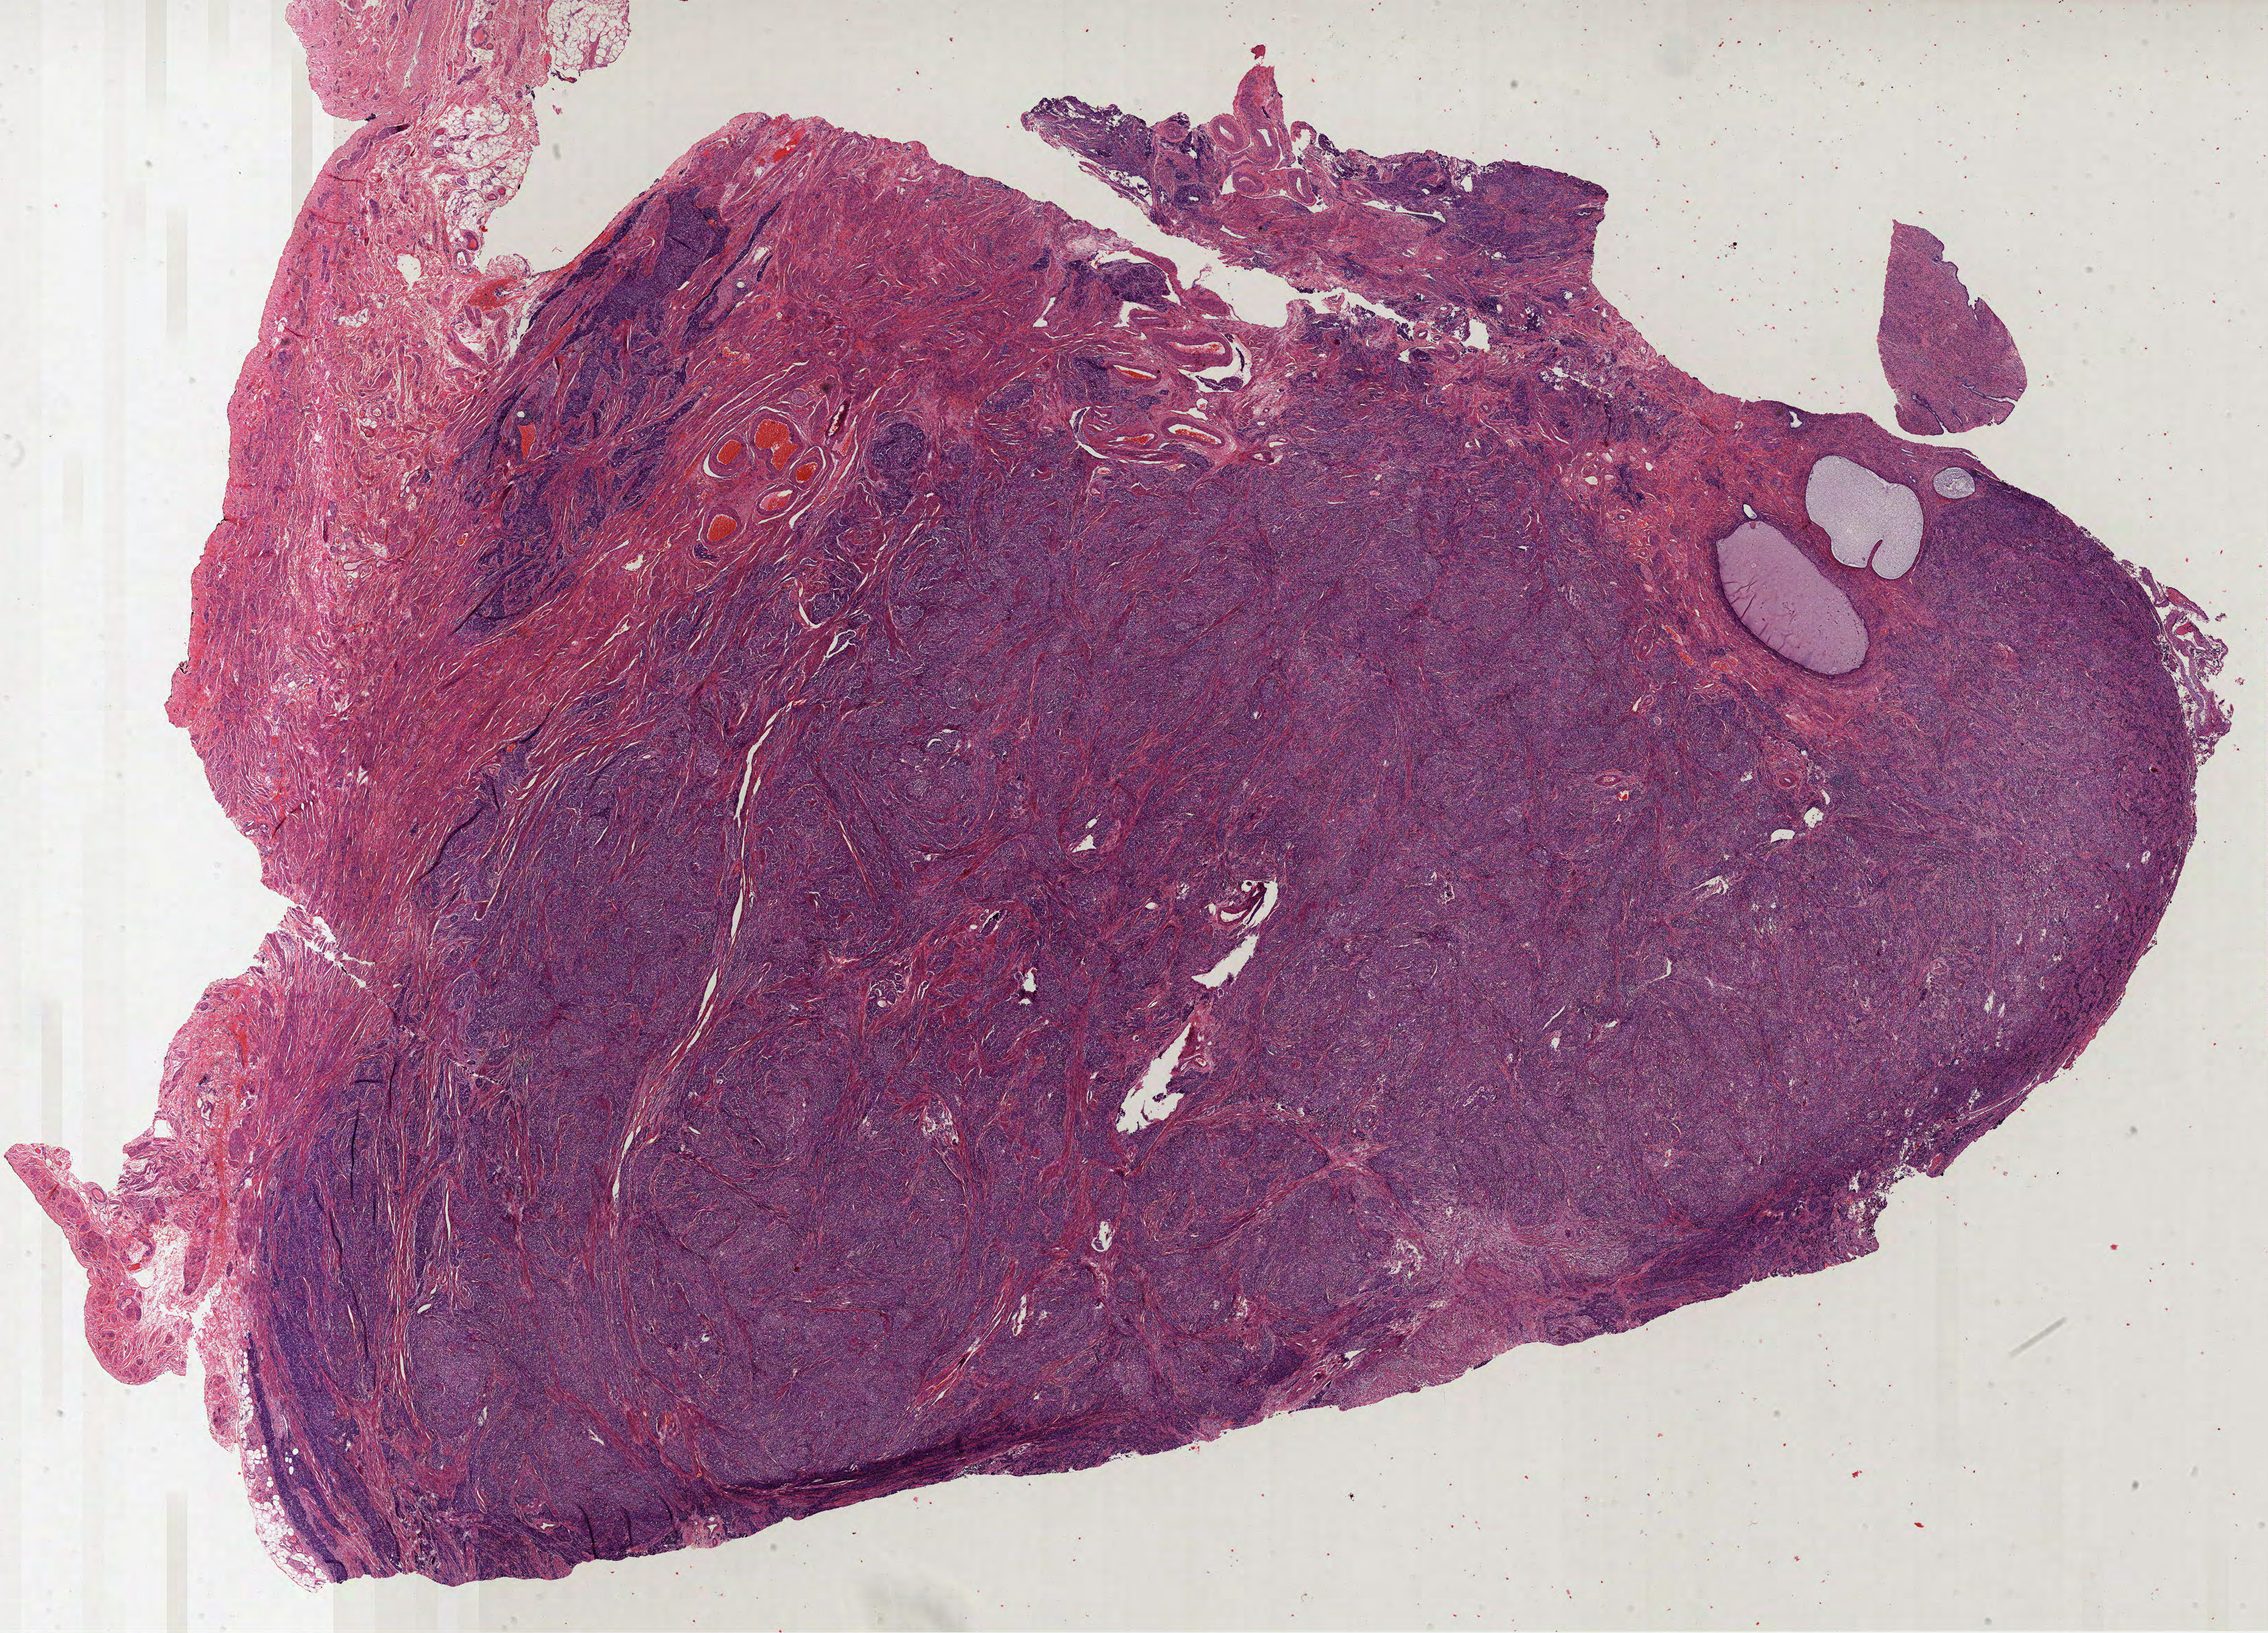
Digitized H&E tissue section (whole slide), low-resolution overview of the scanned area, about 26.3 x 19.0 mm (from a 40x scan); FFPE section; uterus, primary tumour sample. Patient: female, age at initial diagnosis 52 years. Histologic grade: G3 (poorly differentiated).
FIGO stage: II. Lymph nodes positive (case pathology): 0 of 7 examined. Pathologic diagnosis: Endometrioid adenocarcinoma, NOS (endometrium).